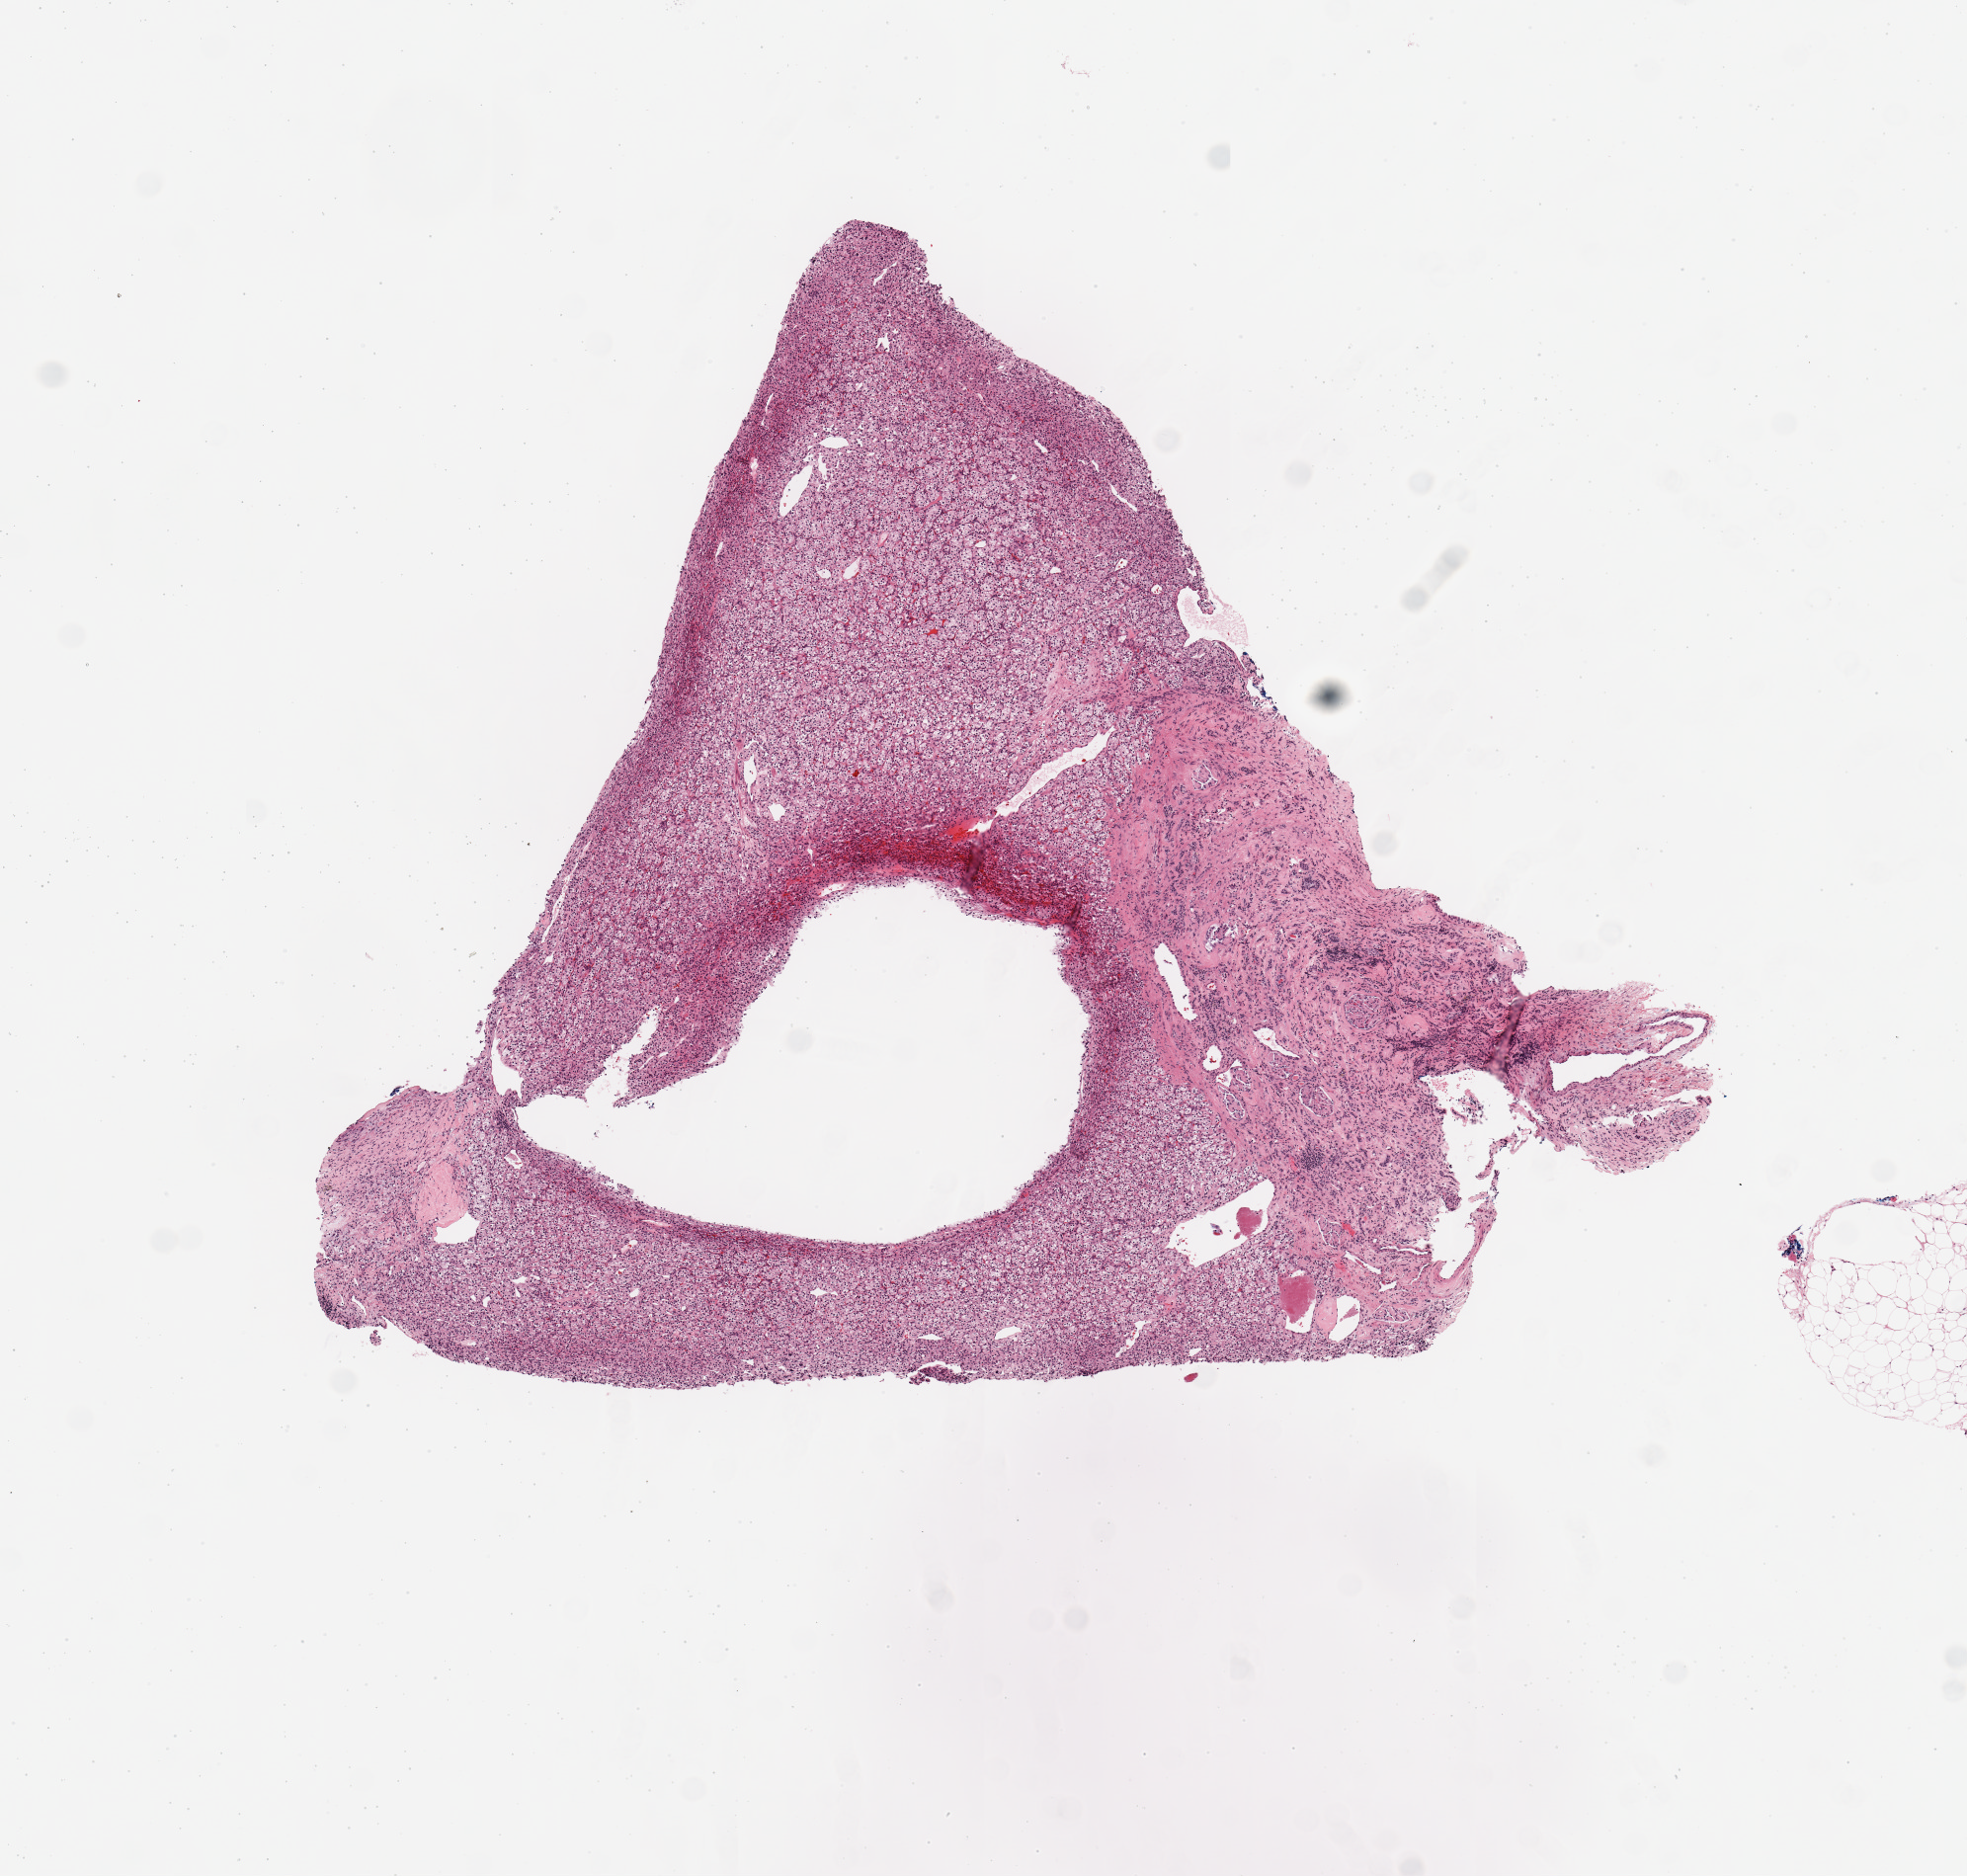
Digitized Hematoxylin and eosin (H&E) stained tissue section (whole slide), shown as a low-resolution overview of the whole scanned area (about 7.9 x 7.5 mm). Tumour tissue sample, kidney. 70-year-old female patient. Histologic grade: G1 (well differentiated).
AJCC pathologic stage: I. Primary tumour site (as recorded): middle. Histologic diagnosis: Renal cell carcinoma, NOS.